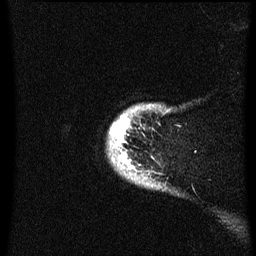
Breast MRI (dynamic contrast-enhanced), one sagittal slice; position 57 of 60 along the scan axis; dynamic contrast-enhanced series, image 2 of 3 at this slice position (ordered by acquisition); 1.5 T; TE 4.2 ms, TR 8.4 ms; 2.3 mm slice thickness; 256 × 256 image matrix, field of view 200 × 200 mm. Female patient, age 38 years. Case-level facts recorded for this patient, not image findings: setting: breast cancer imaged before/during neoadjuvant chemotherapy; receptor status: HER2-positive.
Outlined on this slice (semi-automatically segmented with operator editing):
- analysis volume of interest (the breast-tissue region the enhancement analysis was run in; not a lesion): bounding box (x1, y1, x2, y2) in pixels: (108, 104, 169, 191)
- tumour enhancement mask (voxels above the 70 % enhancement threshold inside the analysis volume of interest): (111, 116, 130, 163)